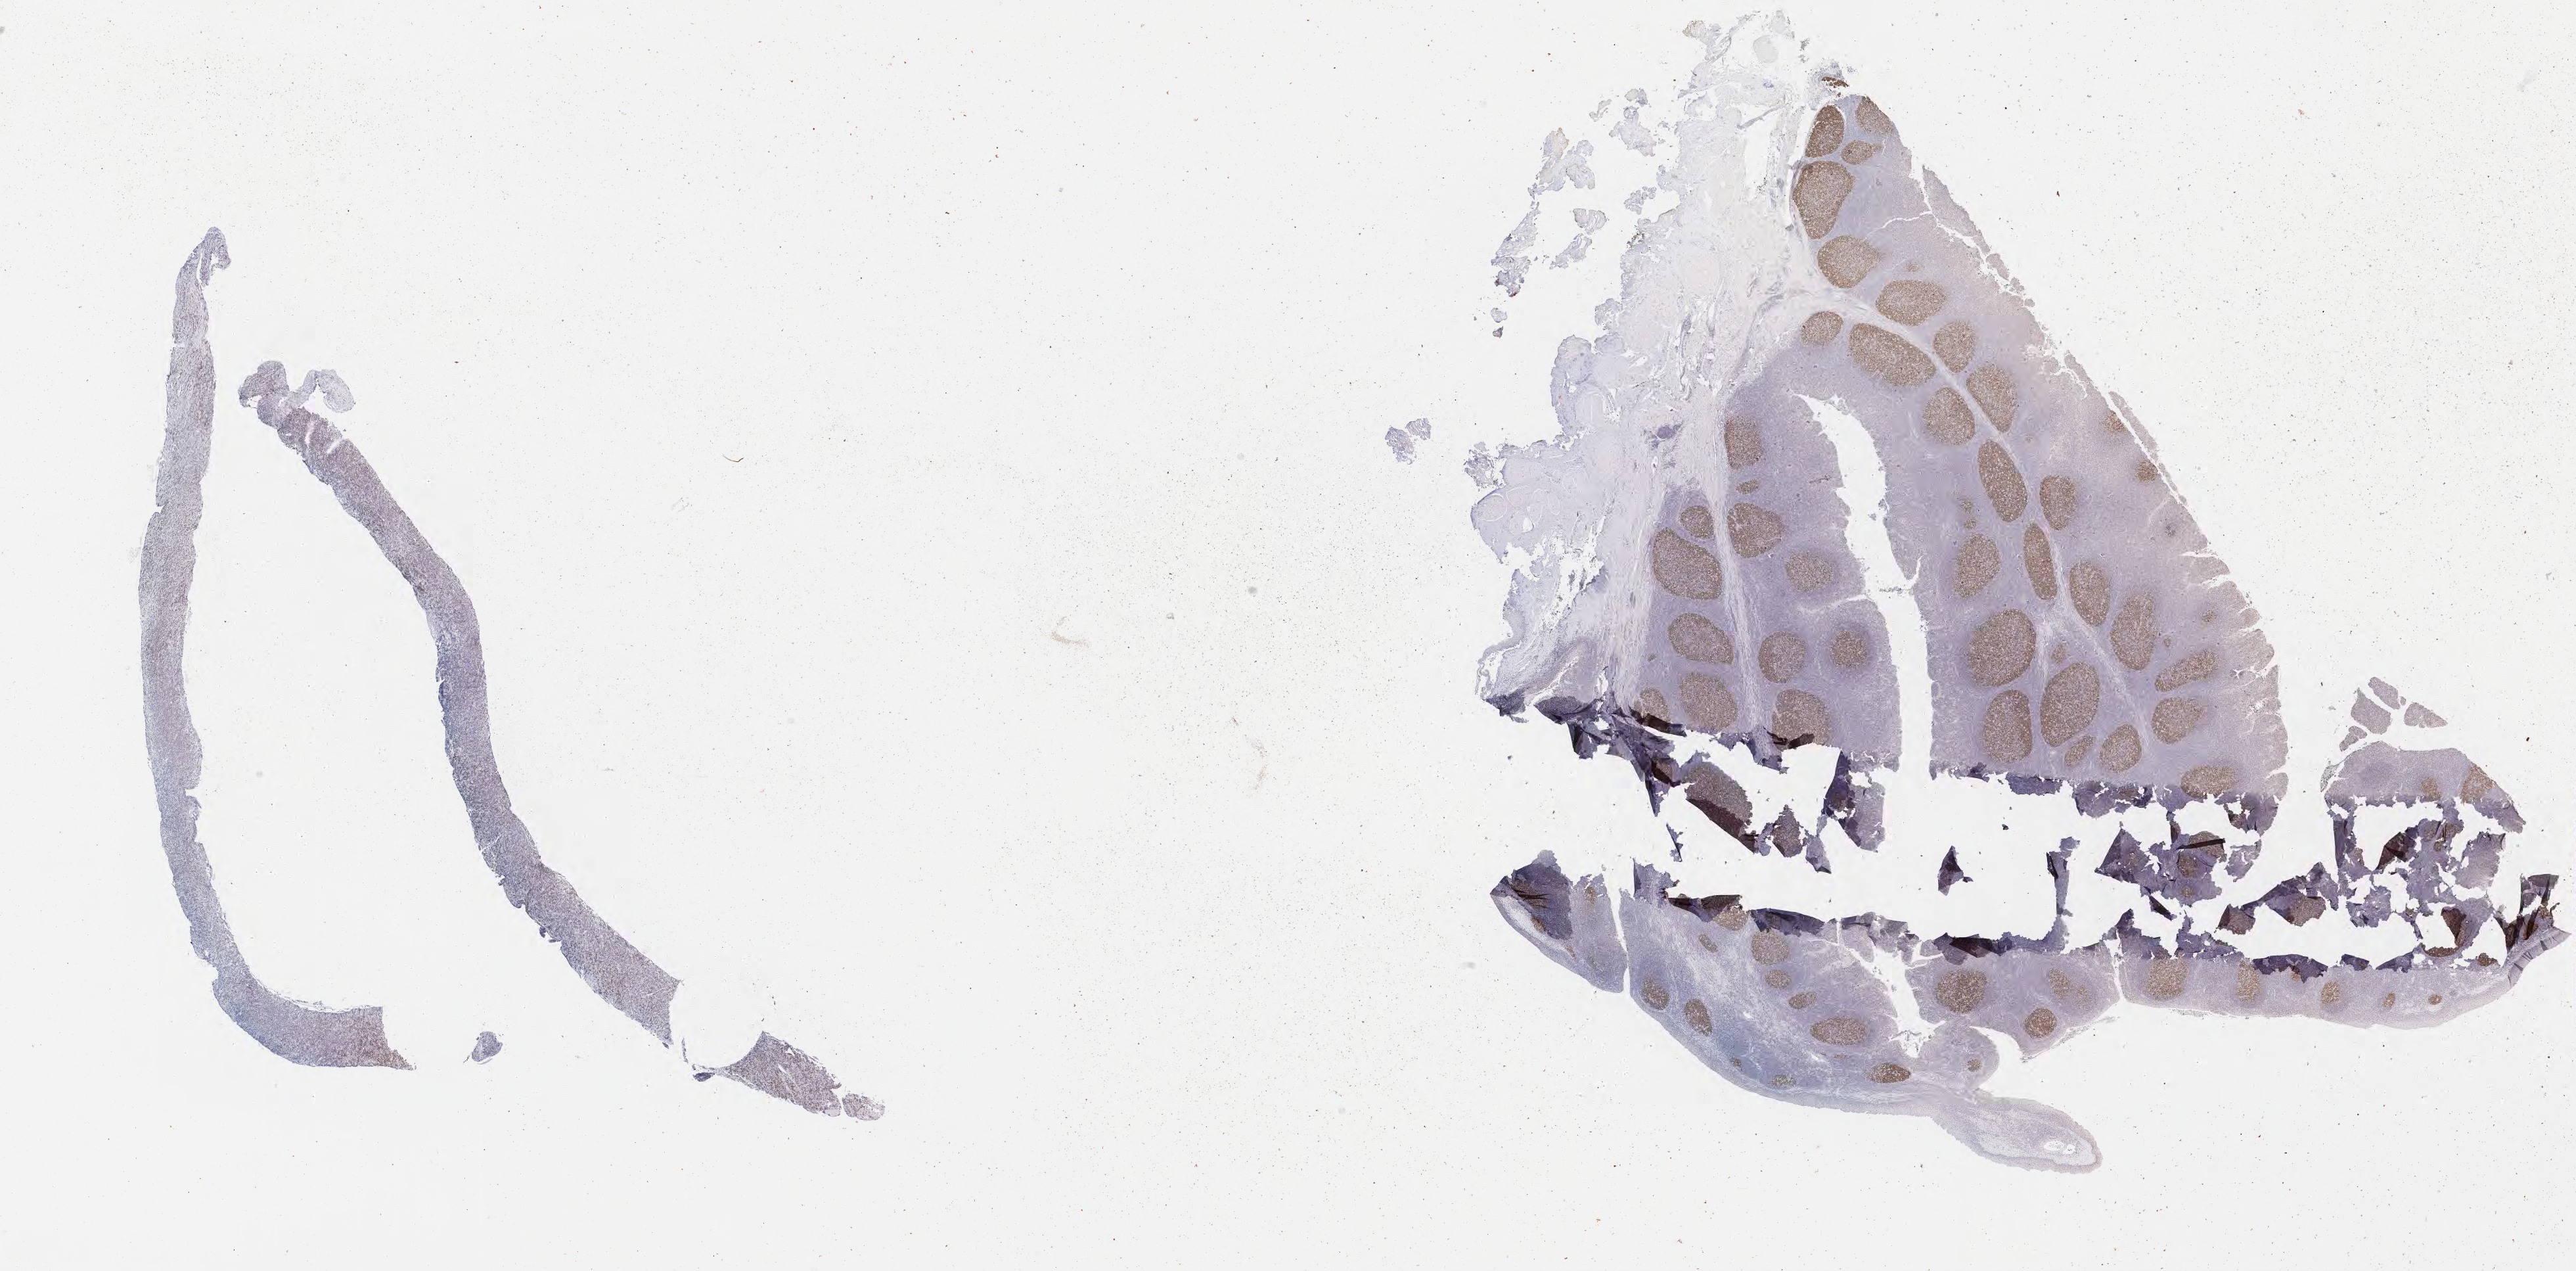
IHC for BCL6, whole-slide image, whole scanned area (about 31.7 x 15.6 mm) shown as a low-resolution overview. Tumor tissue. Anatomic site: abdomen proper. Male, age 9 years at initial diagnosis.
Histologic diagnosis: Burkitt lymphoma, NOS.